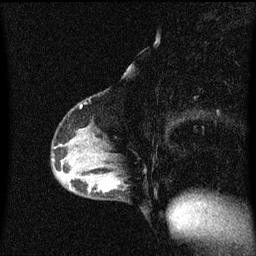
Breast MRI (dynamic contrast-enhanced), one sagittal slice. Slice 31 of 60 in the series (ordered by position). Dynamic contrast-enhanced series, image 2 of 3 at this slice position (ordered by acquisition). 1.5 T. TE 4.2 ms, TR 8.4 ms. 2 mm slice thickness. 256 × 256 image matrix, field of view 200 × 200 mm. Patient: female, 40 years.
Structures marked on this image (semi-automatically segmented with operator editing):
- analysis volume of interest (the breast-tissue region the enhancement analysis was run in; not a lesion): box from (x=82, y=172) to (x=127, y=201) px
- tumour enhancement mask (voxels above the 70 % enhancement threshold inside the analysis volume of interest): (x=106, y=182)–(x=120, y=191)